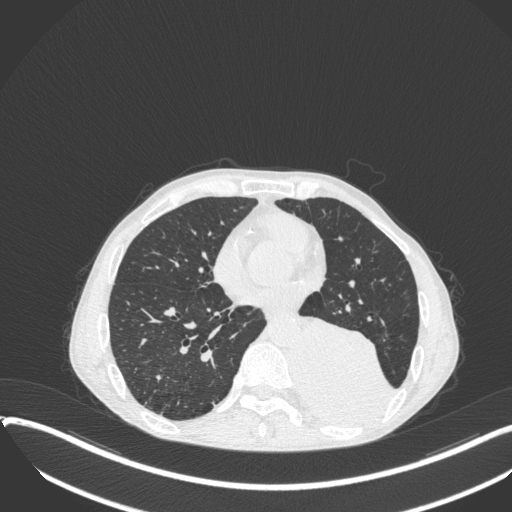
Chest CT, one axial slice. Position 145 of 400 along the scan axis. Lung window (W 1500 / L -600 HU). 1 mm slice thickness. 512 × 512 image matrix. Patient: male, 57 years. From the clinical record (not read from this slice): clinical TNM (as recorded): T4 N0 M0.
Annotated regions visible in this slice (rectangle marked by the reading radiologist):
- lung tumour (recorded histology: squamous cell carcinoma): box from (x=292, y=308) to (x=393, y=428) px